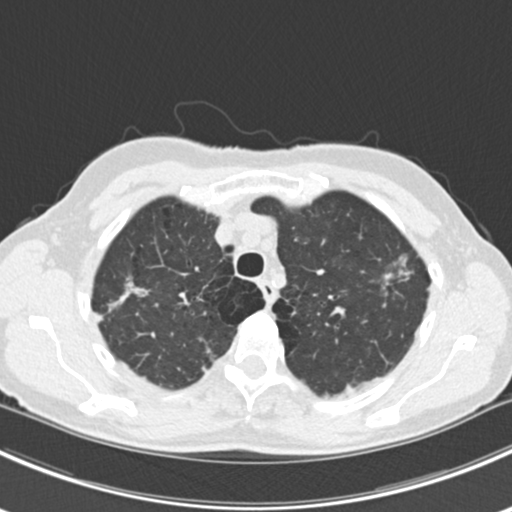
Axial slice from a low-dose chest CT screening exam, baseline screening round, lung window (W 1500 / L -600 HU), 120 kVp, slice 42 of 224 in the series, 512 × 512 image matrix. Female, age 63 years at enrolment. Current smoker at enrolment.
Lesion marked by an expert reader, bounding box [x1, y1, x2, y2] px = [365, 244, 432, 311]. The screening reader recorded 10 non-calcified nodules or masses ≥4 mm on this exam (right lower lobe, right lower lobe, left lower lobe, left lower lobe, right middle lobe, right lower lobe, left lower lobe, left upper lobe, right upper lobe, left upper lobe); which of them this box marks is not recorded. Lung cancer was diagnosed 751 days after this screen: bronchiolo-alveolar adenocarcinoma, NOS, right upper lobe, right middle lobe, right lower lobe, left upper lobe, left lower lobe, moderately differentiated (G2), stage IV (AJCC 6th edition).